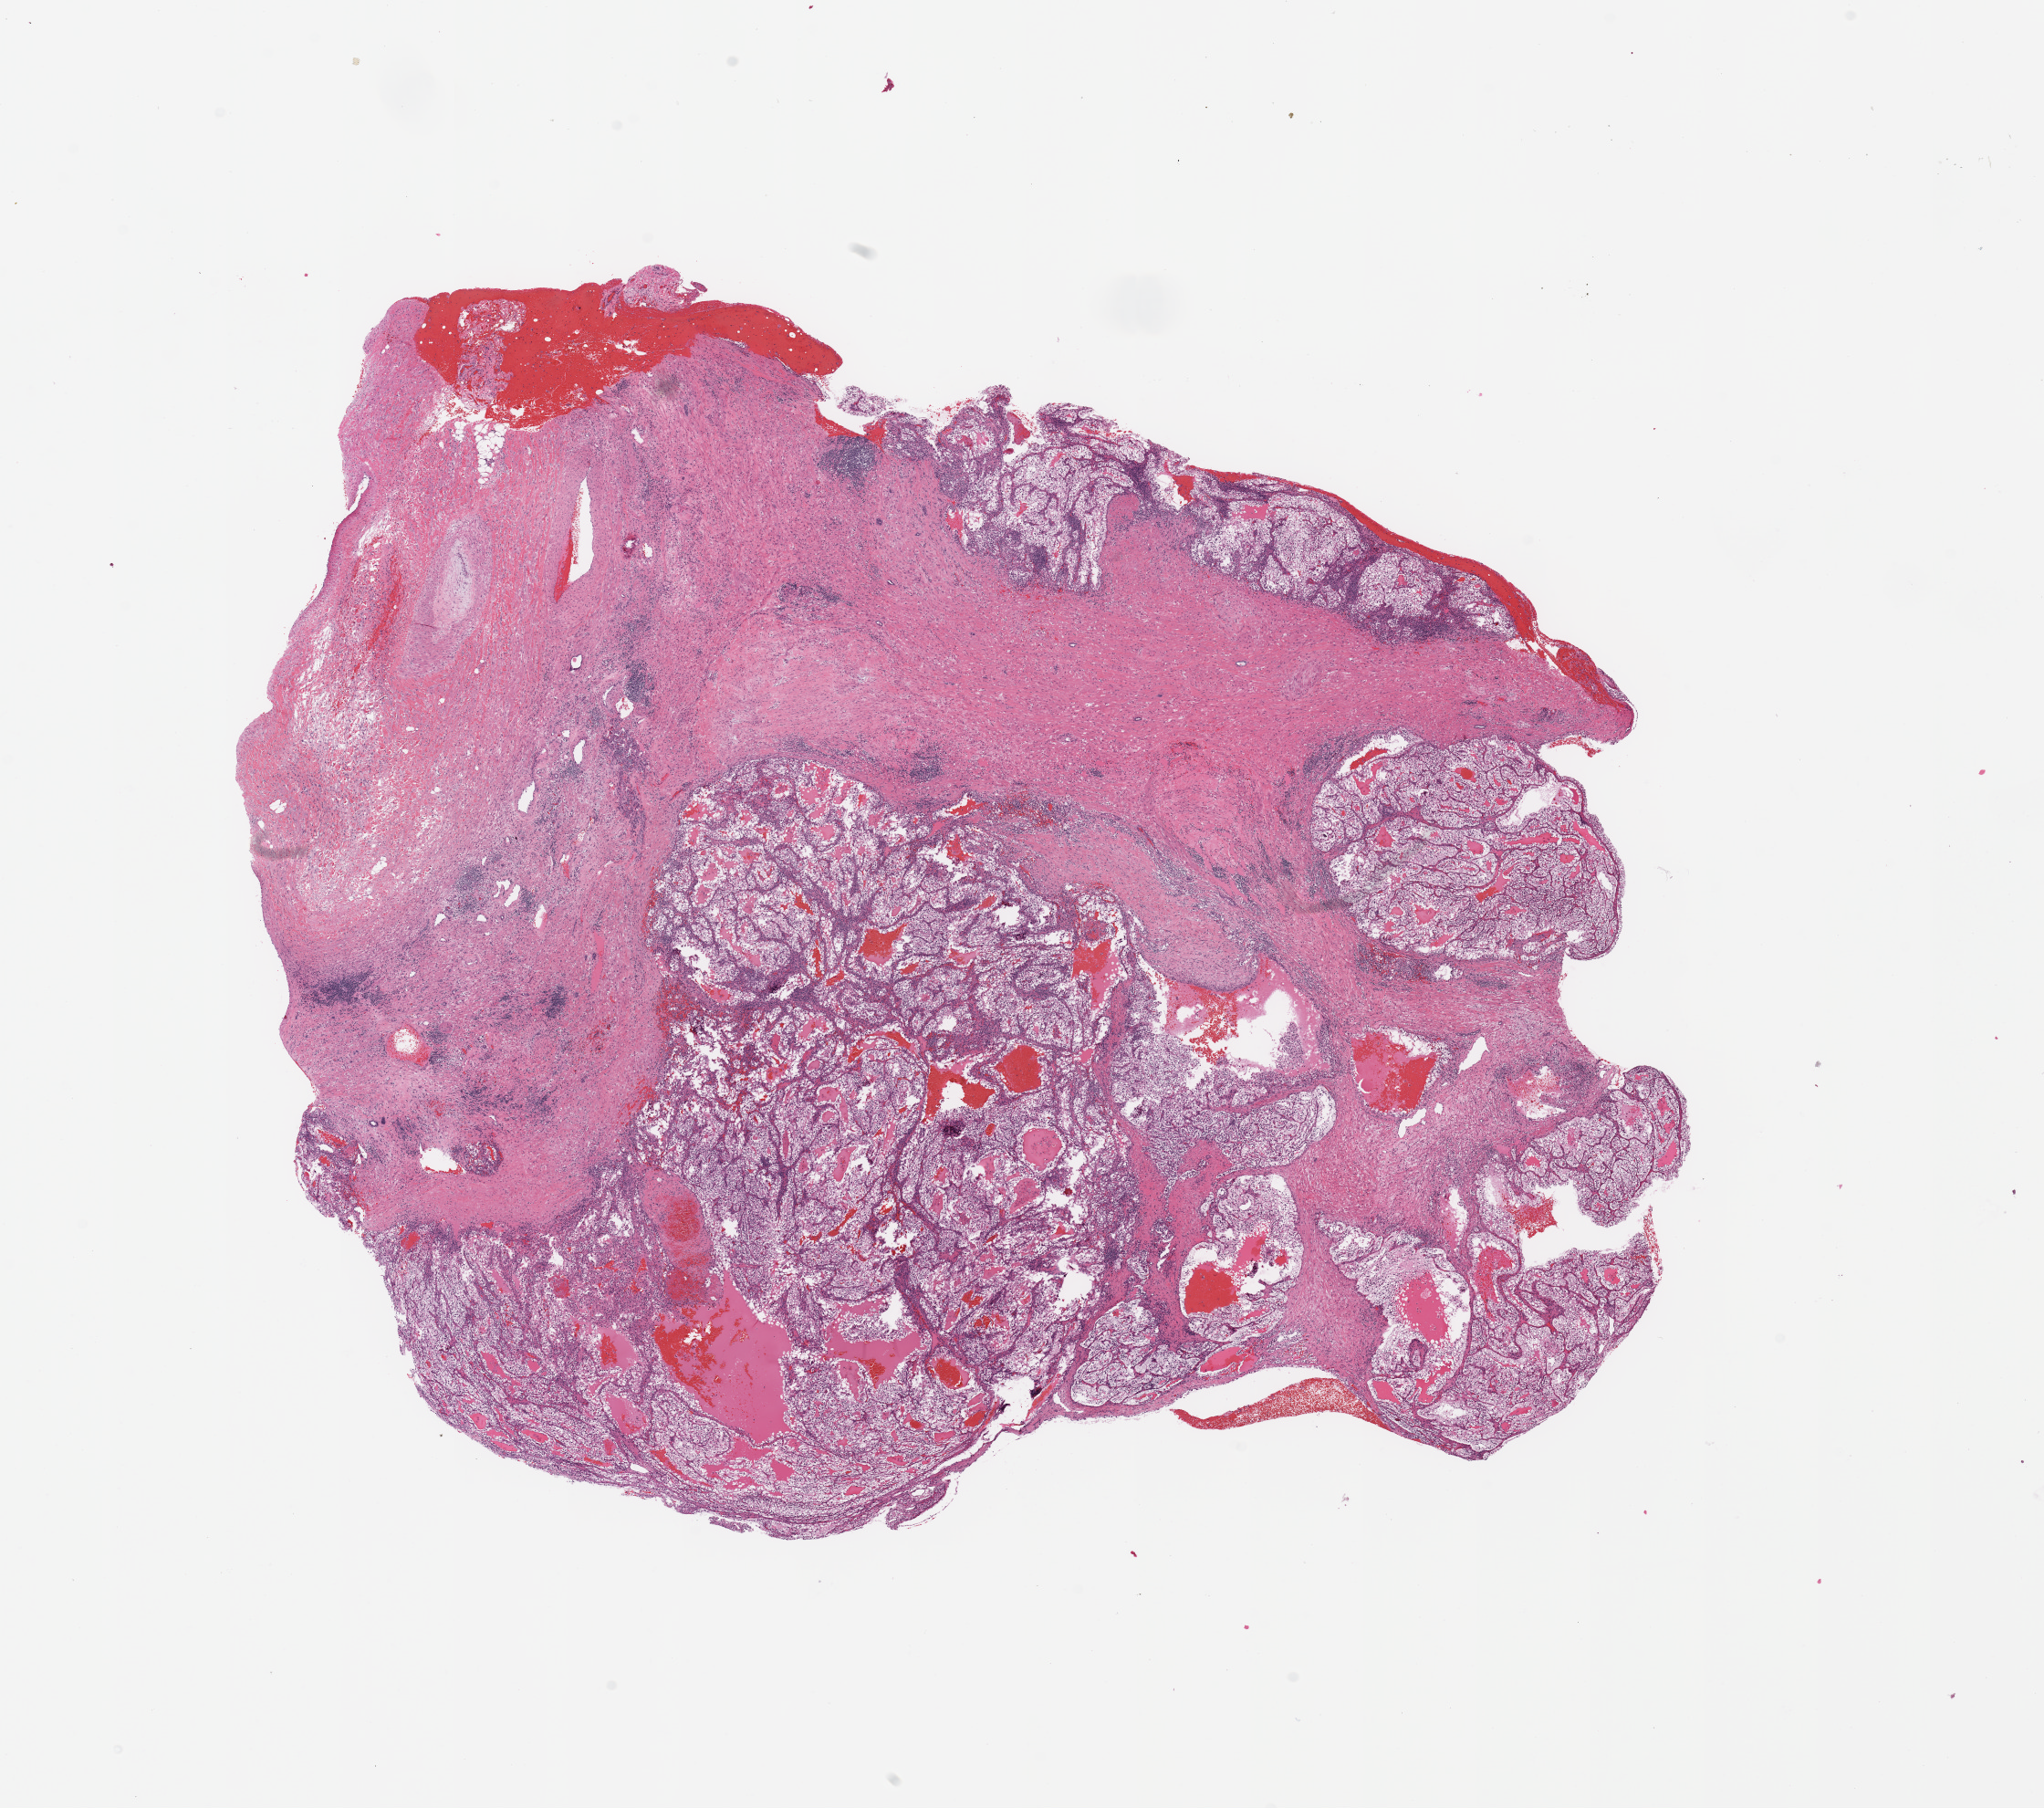
Whole-slide histology image, H&E-stained, shown as a low-resolution overview of the whole scanned area (about 17.7 x 15.7 mm, acquisition: 20x scan), kidney, tumour tissue. 55-year-old male patient. Histologic grade: G3 (poorly differentiated).
• diagnosis: Renal cell carcinoma, NOS
• AJCC pathologic stage: IV